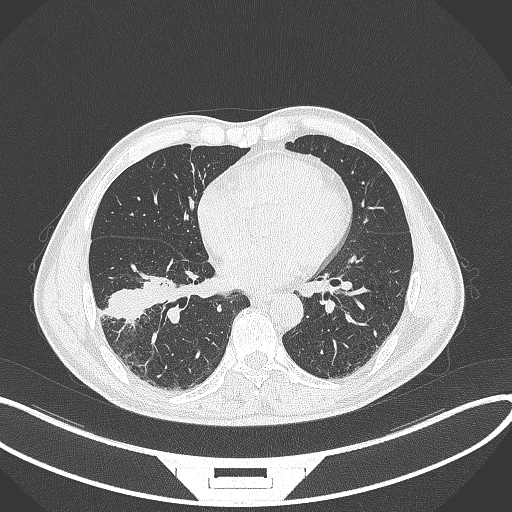
Chest CT, one axial slice. Reconstruction kernel B70f. Lung window (W 1500 / L -600 HU). 1 mm slice thickness. 512 × 512 image matrix, field of view 400 × 400 mm. Patient: male, 58 years. Case-level facts recorded for this patient, not image findings: clinical TNM (as recorded): T3 N0 M0.
Structures marked on this image (rectangle marked by the reading radiologist):
- lung tumour (recorded histology: squamous cell carcinoma): box from (x=99, y=269) to (x=177, y=325) px